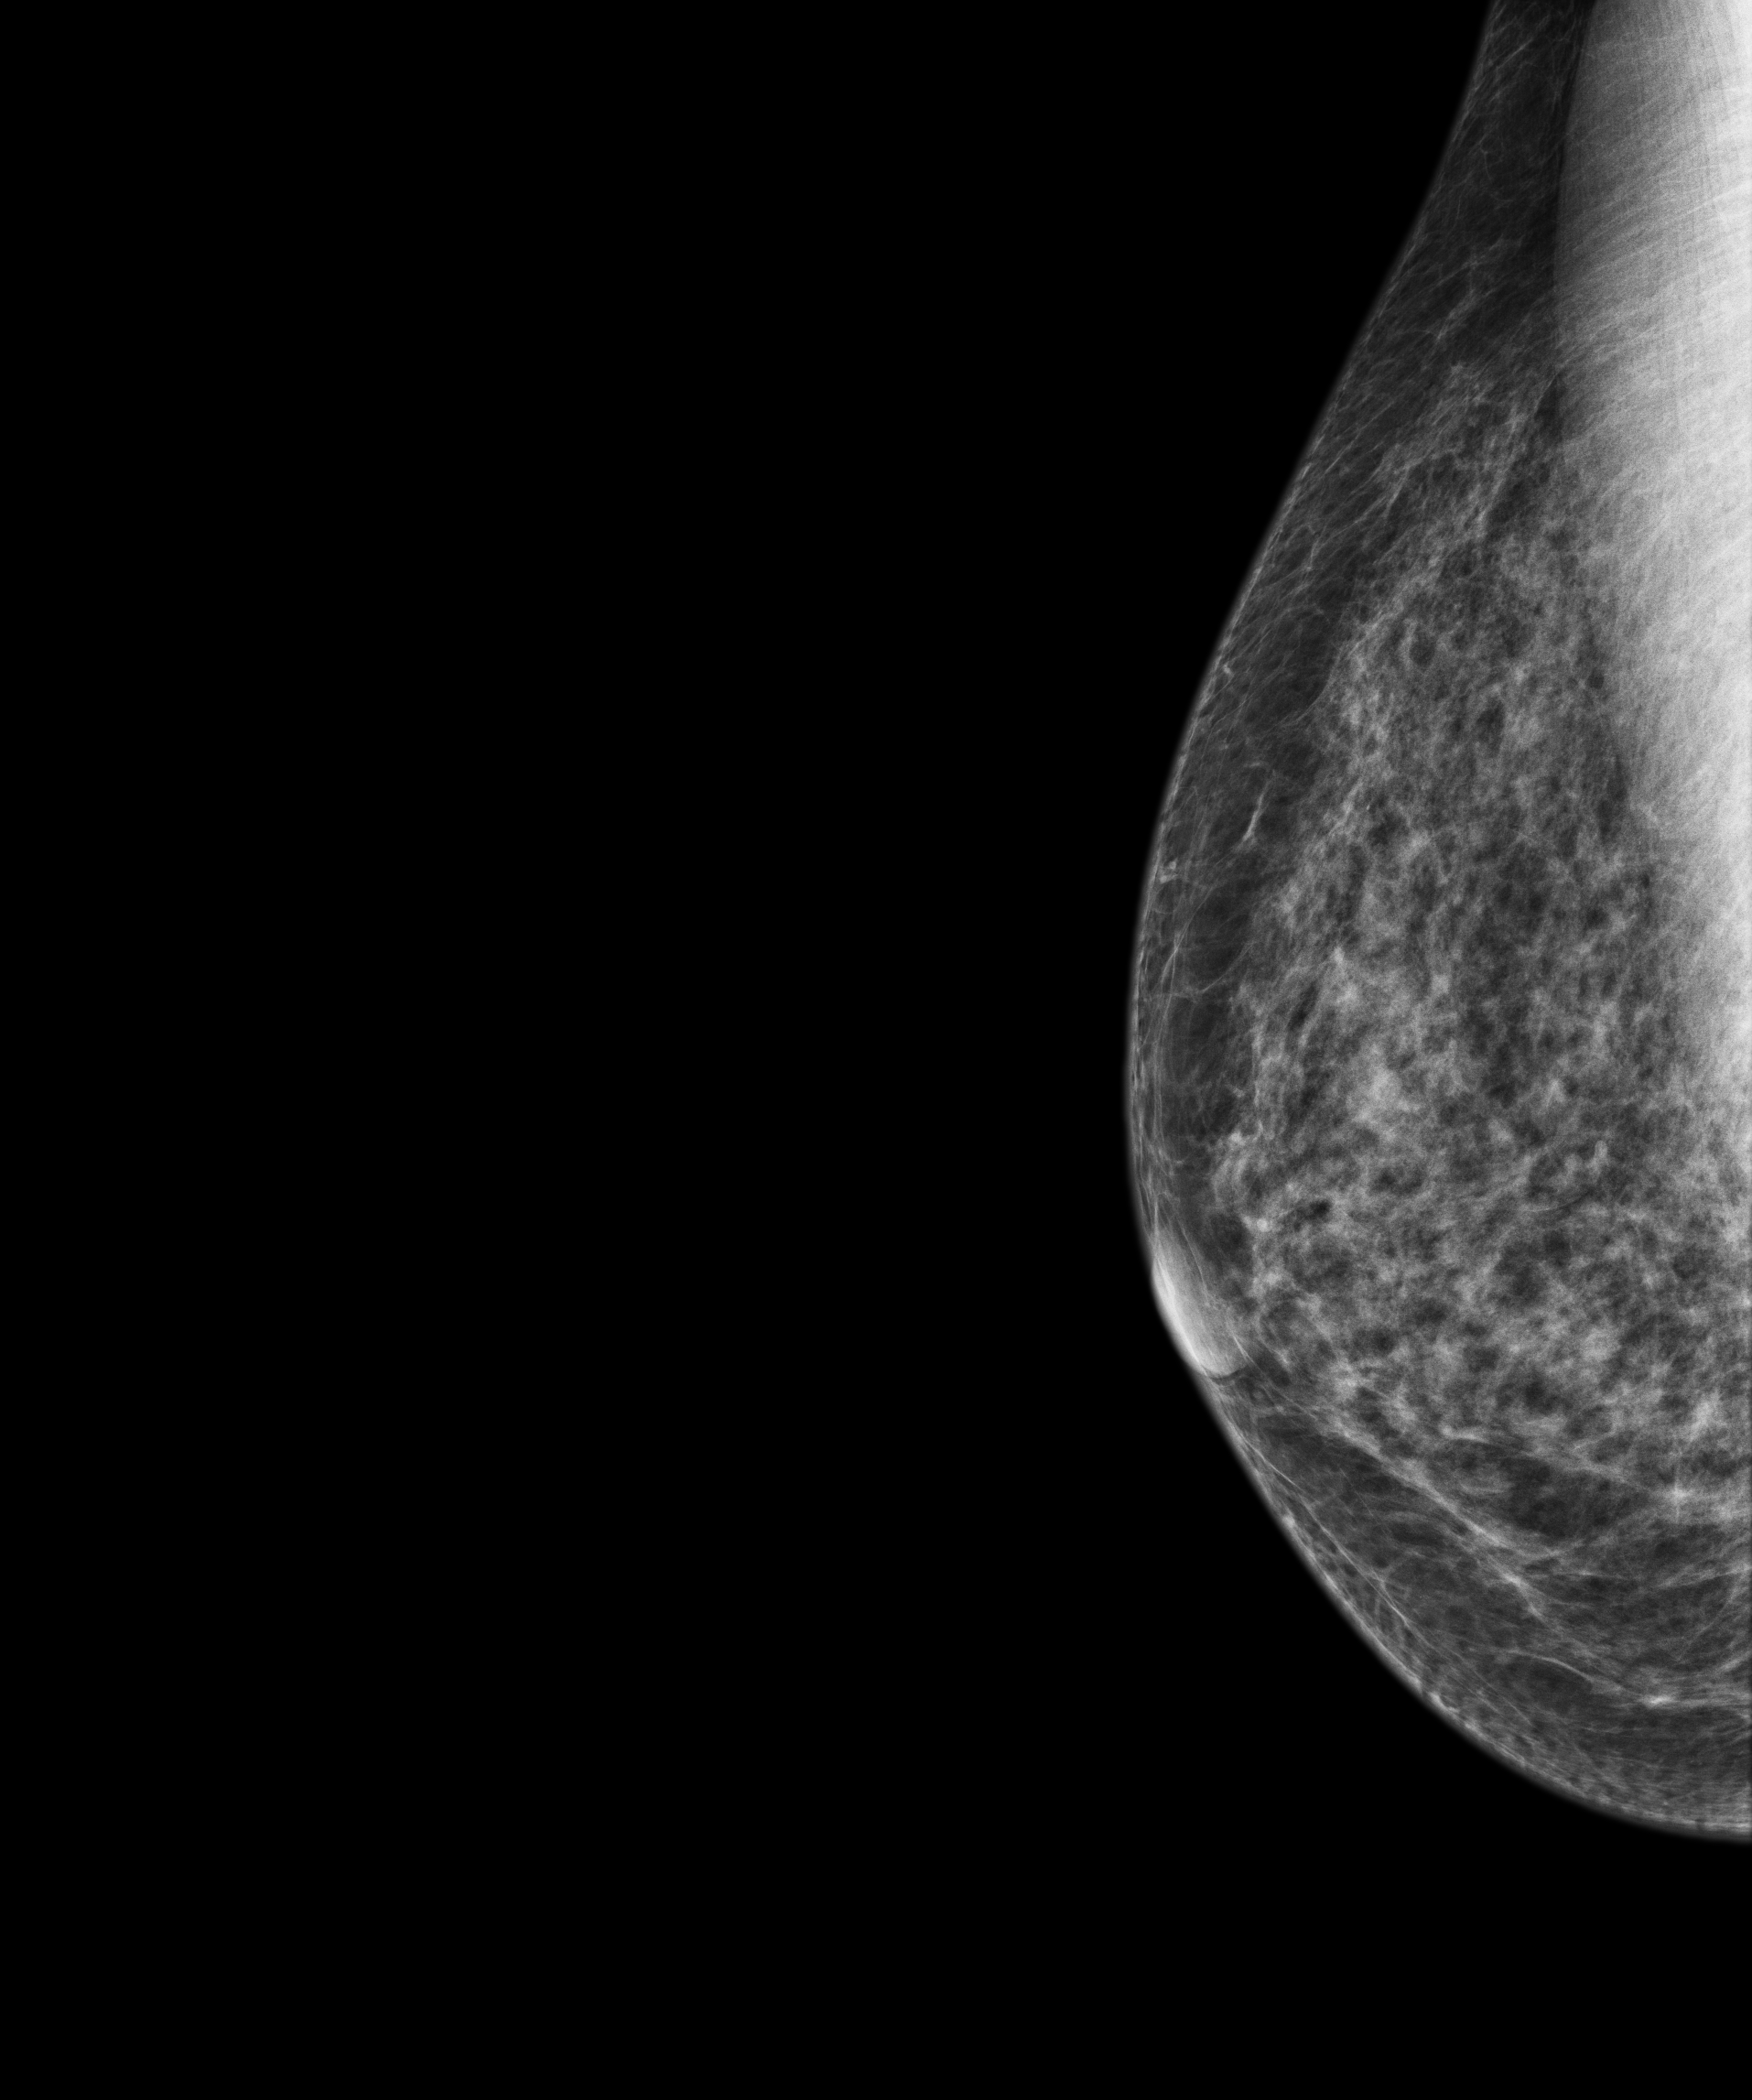
Full-field digital mammogram (FFDM), right breast, laterally exaggerated craniocaudal (XCCL) view, annual screening mammography examination, compressed breast thickness 54 mm. Female patient, age 69 years.
- BI-RADS breast density category at the screening exam (both breasts, scale 1–4): 3
- final BI-RADS category for the screening round (tomosynthesis exam, both breasts): category 1
- recall: no recall after this screen